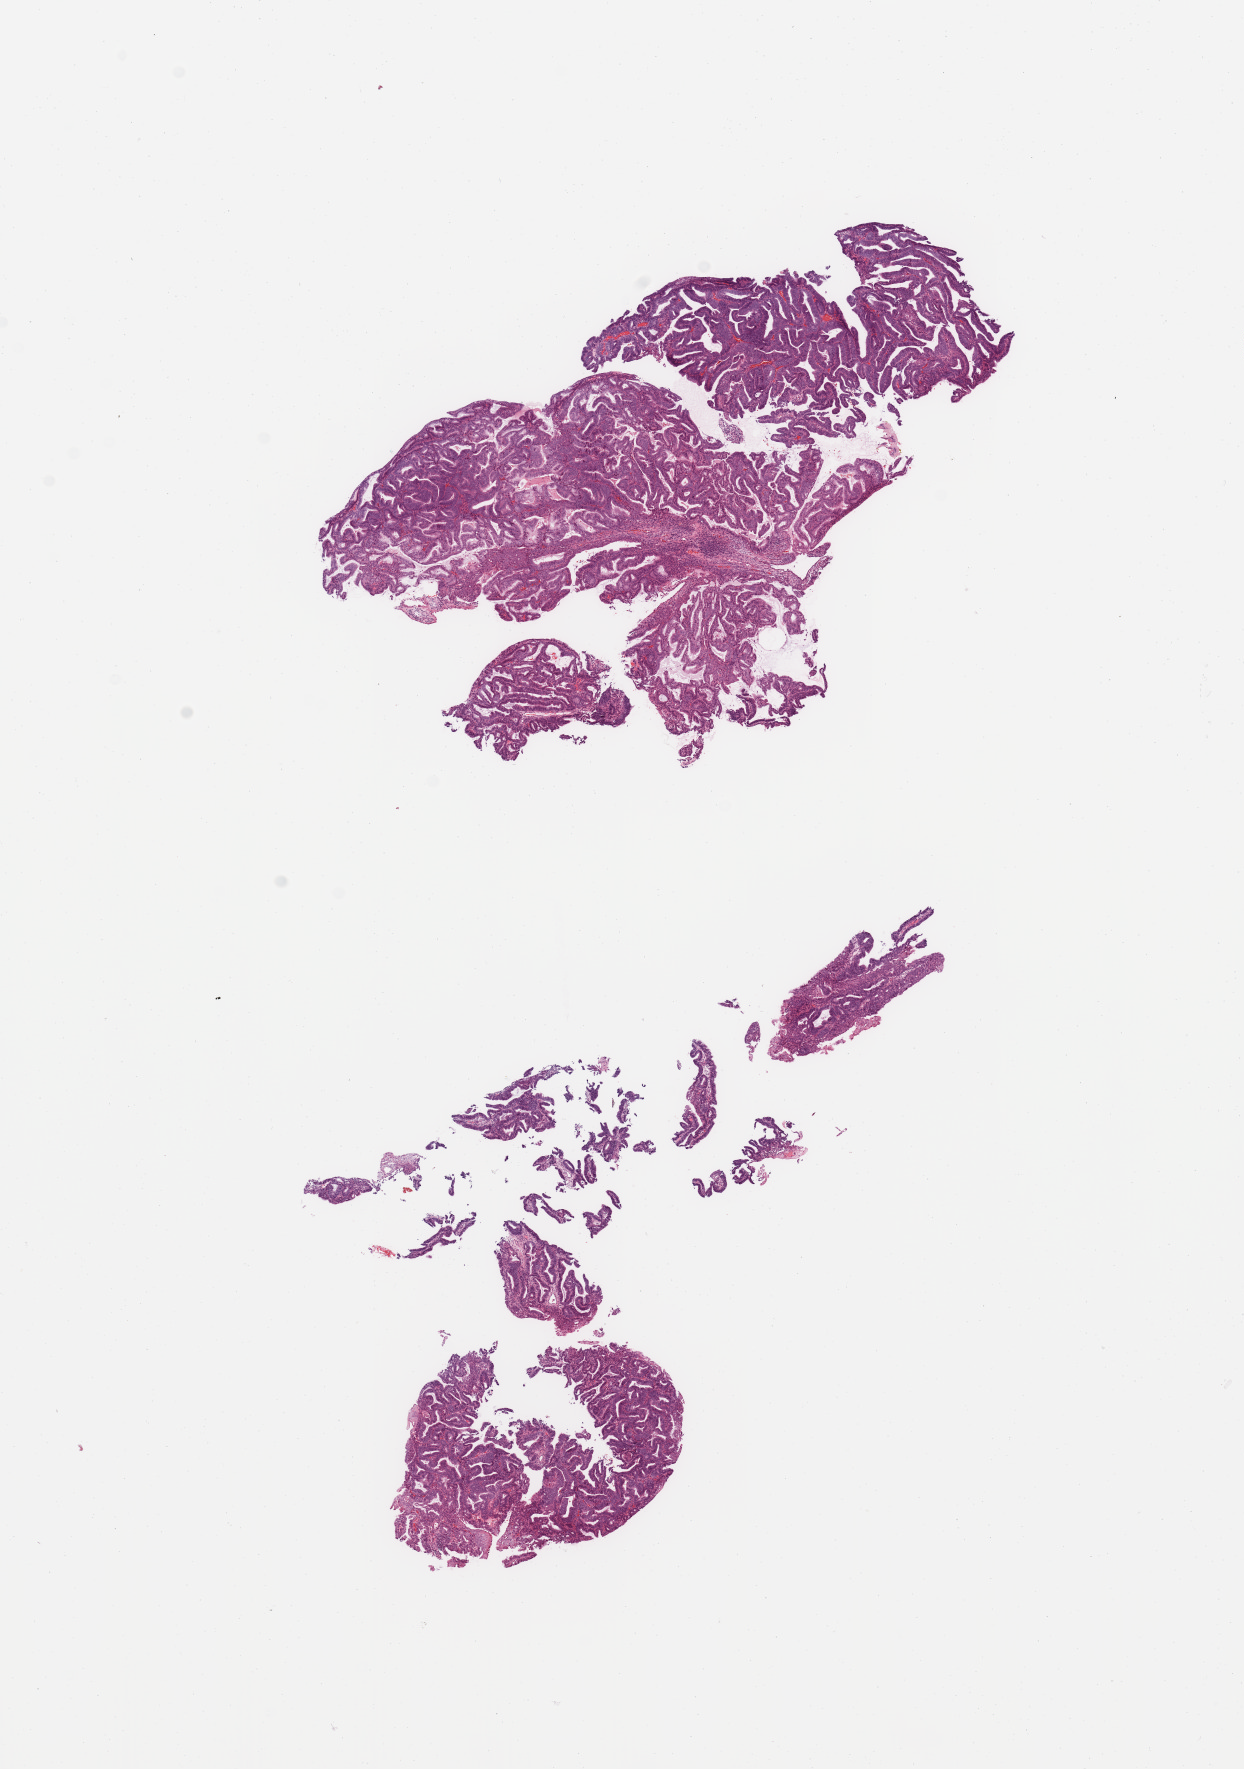
Whole-slide histology image, H&E — low-resolution overview of the scanned area, about 9.8 x 14.0 mm (from a 20x scan); tumour tissue sample, sampled site: uterus. Female, 55 y/o. Histologic grade: G1 (well differentiated). Pathologist review of this section (percent, as recorded): tumour nuclei 90%, necrosis 0%.
Diagnosis: Endometrioid adenocarcinoma, NOS. AJCC pathologic stage: IV.